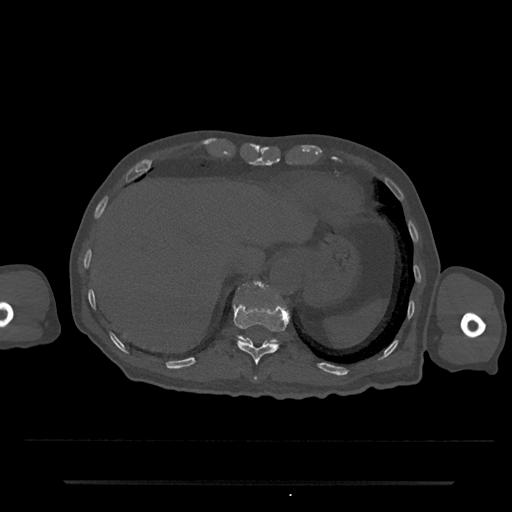
CT including the spine, one axial slice. Slice 245 of 797 in the series (ordered by position). 120 kVp. Bone window (W 1800 / L 400 HU). 0.5 mm slice thickness. 512 × 512 image matrix, field of view 427 × 427 mm. Patient: male, 74 years. Case-level facts recorded for this patient, not image findings: primary cancer: prostate.
Outlined on this slice (semi-automatically segmented with operator editing):
- T11 vertebra: box from (x=233, y=302) to (x=289, y=365) px
- T12 vertebra: (x=237, y=284)–(x=277, y=344)